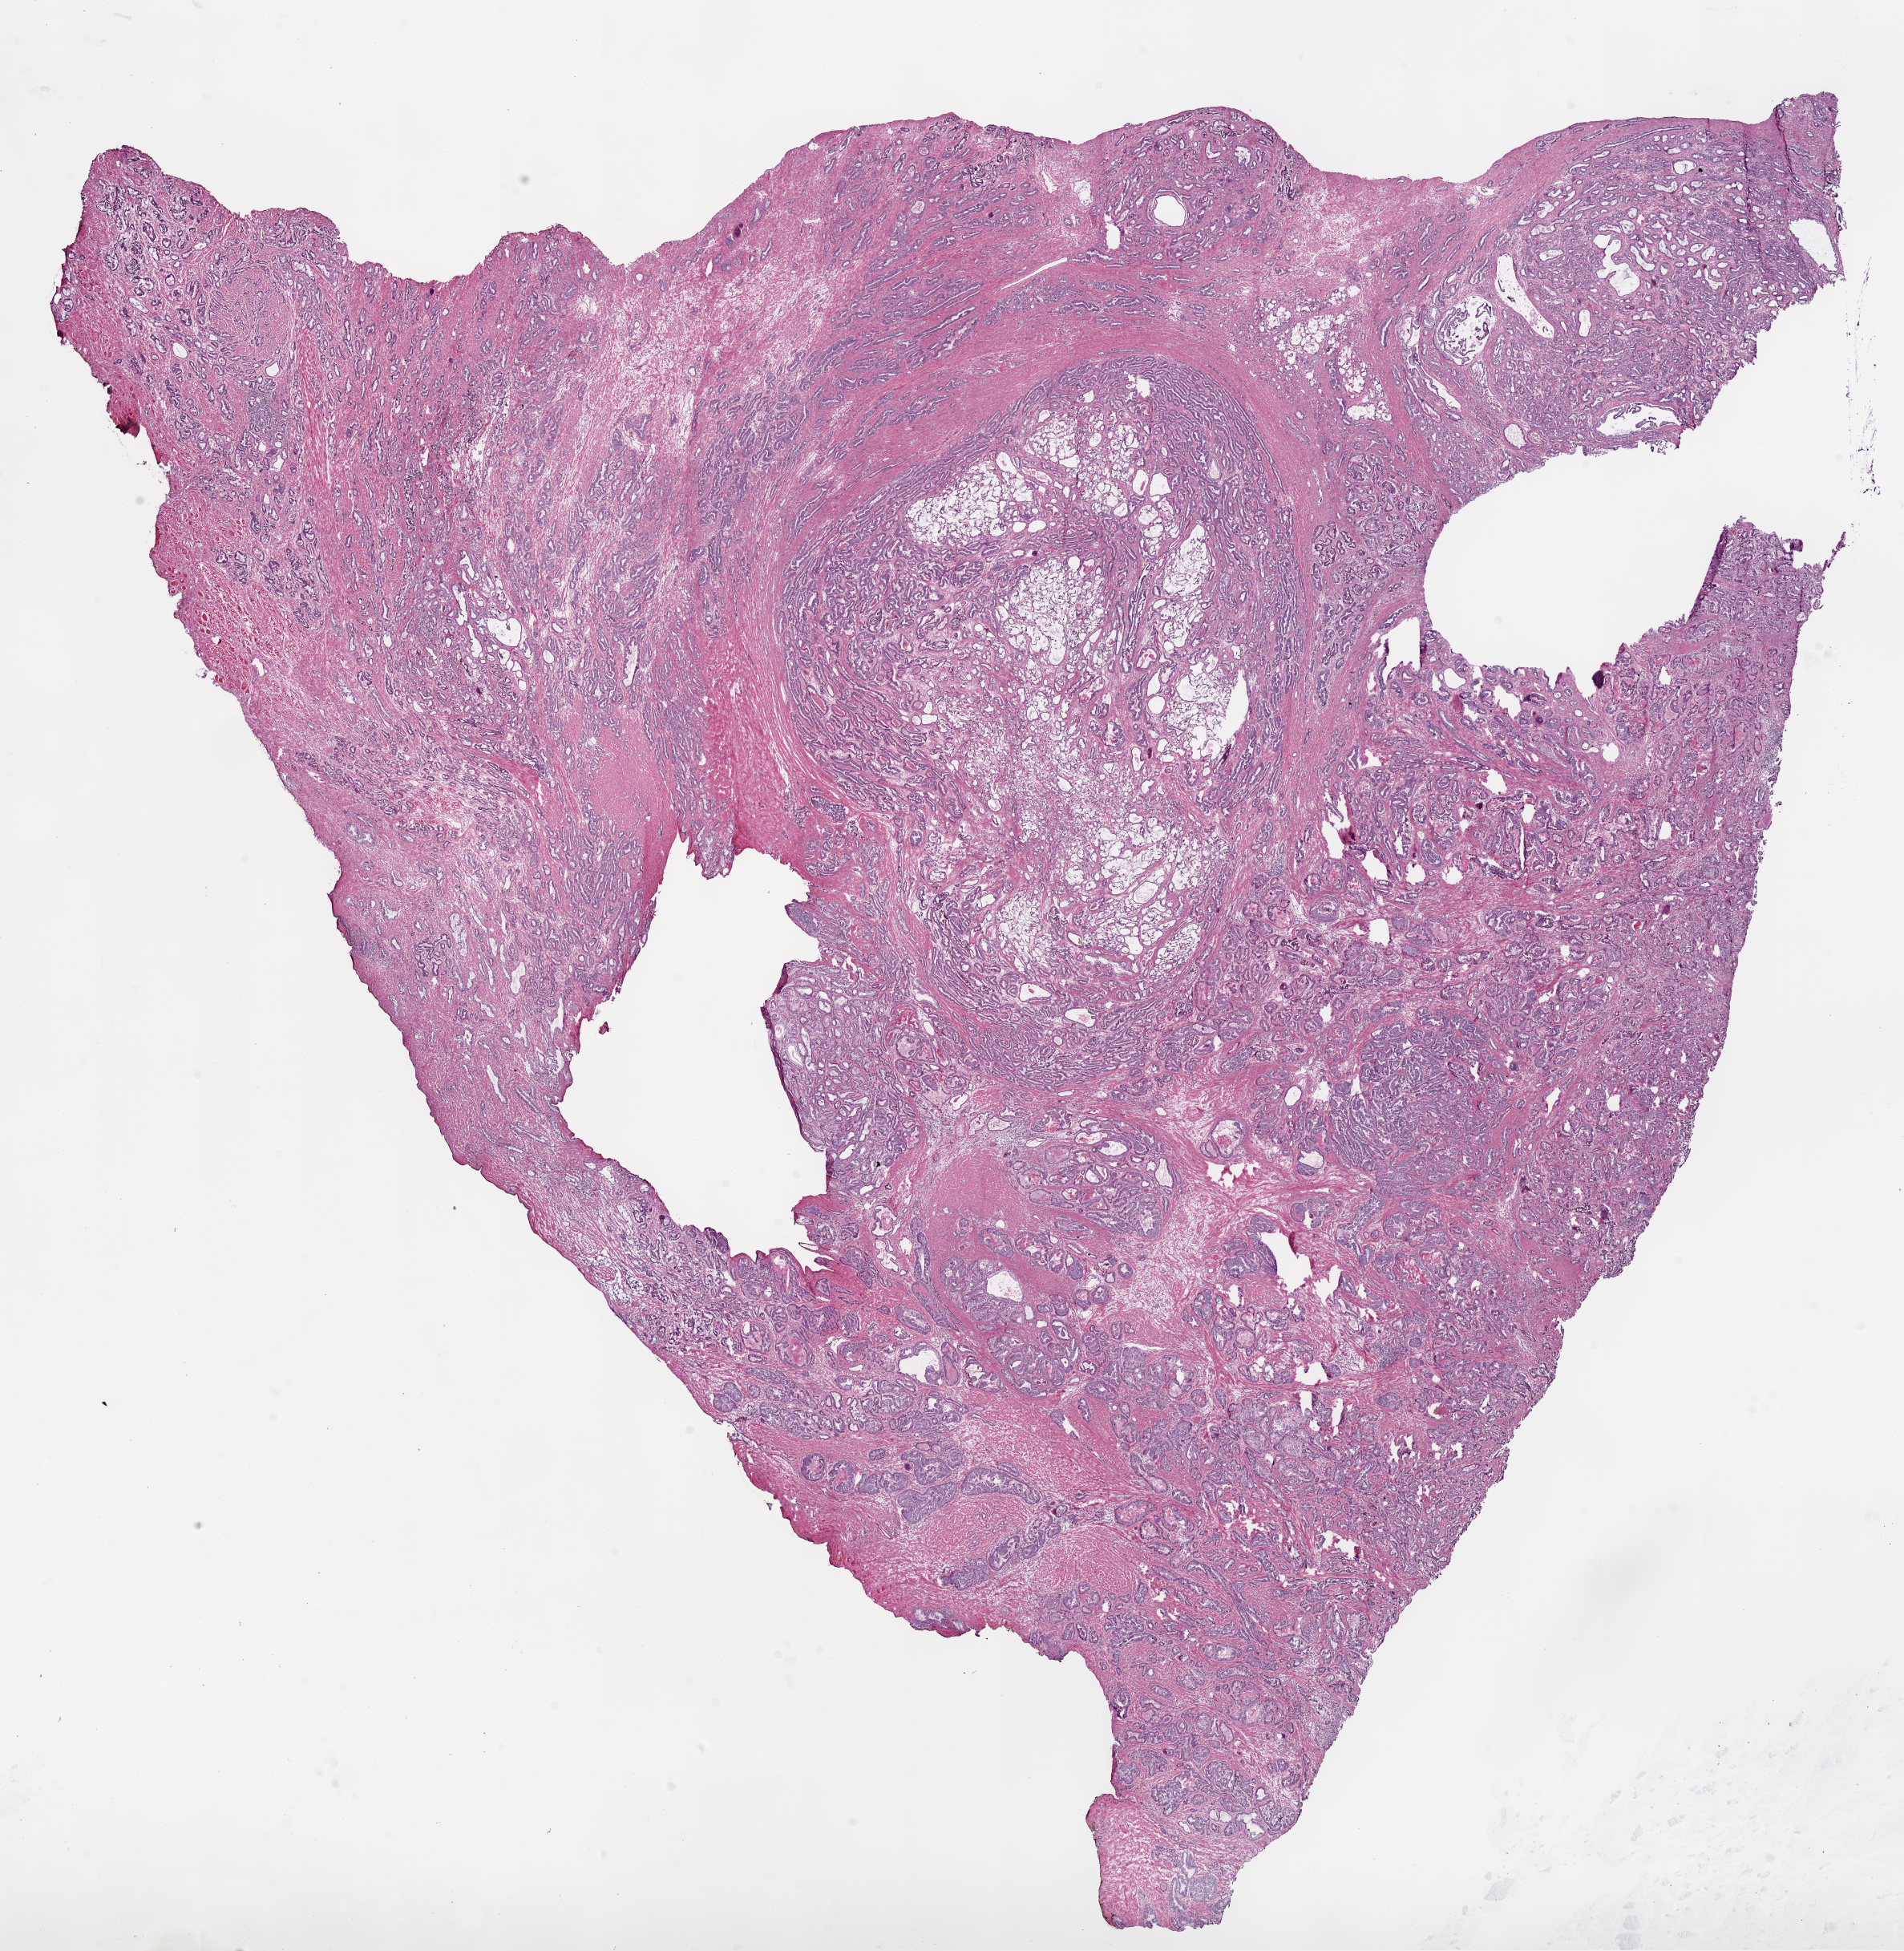
Digitized H&E tissue section (whole slide) — a low-resolution overview of the entire scanned area, about 19.1 x 19.5 mm (from a 20x scan), frozen section from the bottom of the tissue portion, primary tumour sample from the prostate. Patient: male, age at initial diagnosis 61 years. Gleason score: 7 (3+4). Pathologist review of this section (percent, as recorded): tumour cells 70%, tumour nuclei 70%, normal cells 10%, stromal cells 20%, necrosis 0%. Infiltration values recorded for this section: lymphocyte infiltration 2%, monocyte infiltration 0%, neutrophil infiltration 0%.
Laterality: bilateral. Pathologic diagnosis: Acinar cell carcinoma (prostate gland). Lymph nodes positive (case pathology): 0 of 6 examined.